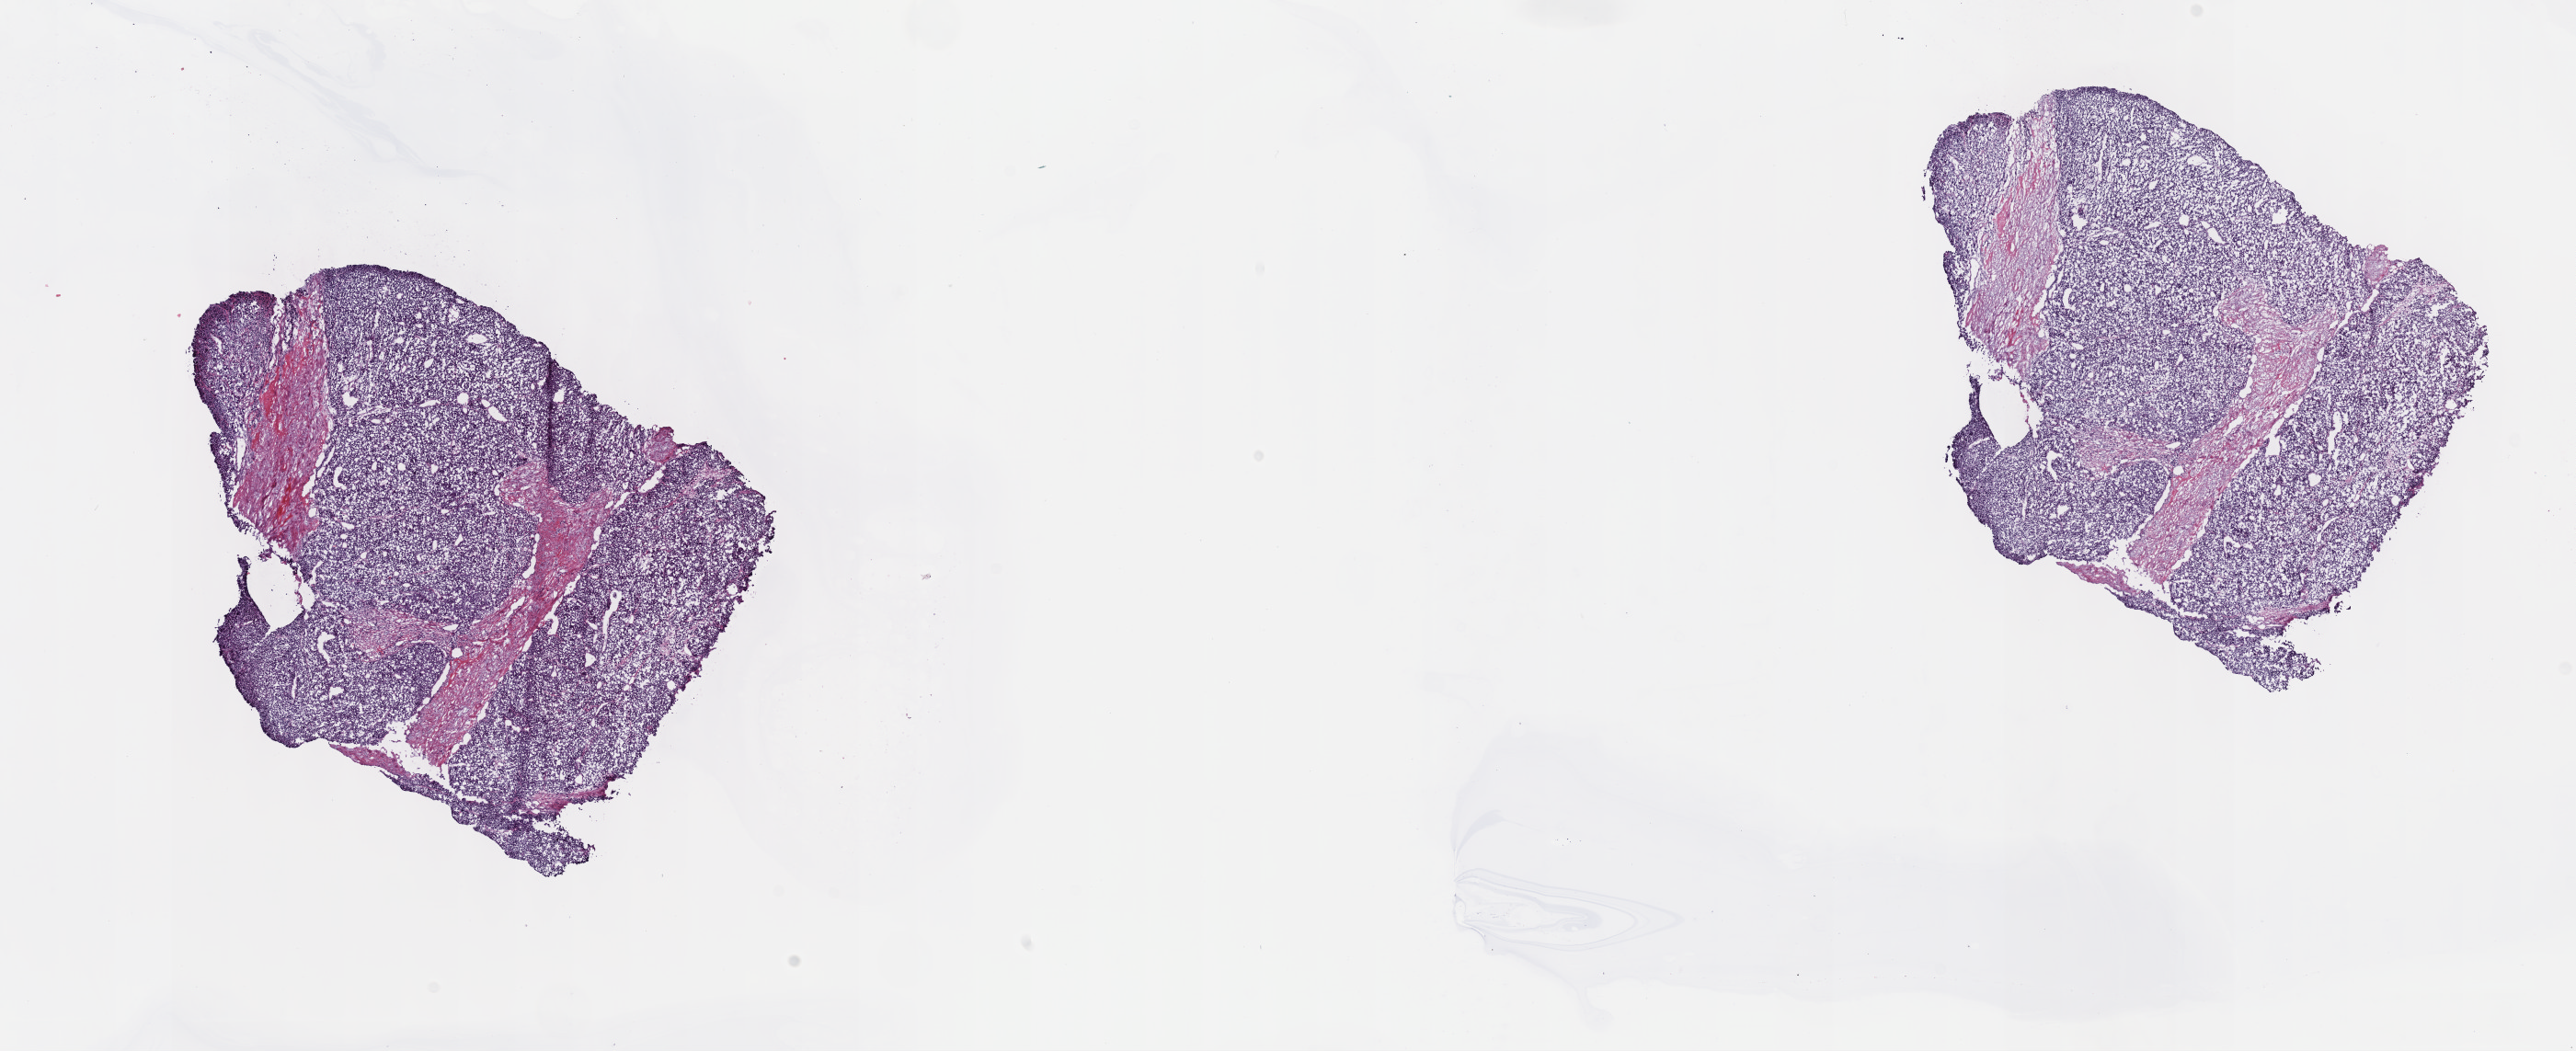
H&E whole-slide image — shown as a low-resolution overview of the whole scanned area (about 22.7 x 9.2 mm, slide scanned at 40x); frozen section from the top of the tissue portion; metastatic tumour sample. Male patient; age at initial diagnosis 79 years. Slide review estimates, as recorded: tumour cells 100%, tumour nuclei 75%, normal cells 0%, stromal cells 0%, necrosis 0%. Infiltration values recorded for this section: lymphocyte infiltration 2%, monocyte infiltration 0%, neutrophil infiltration 0%.
This section: metastatic tumour tissue. Patient diagnosis: Malignant melanoma, NOS.